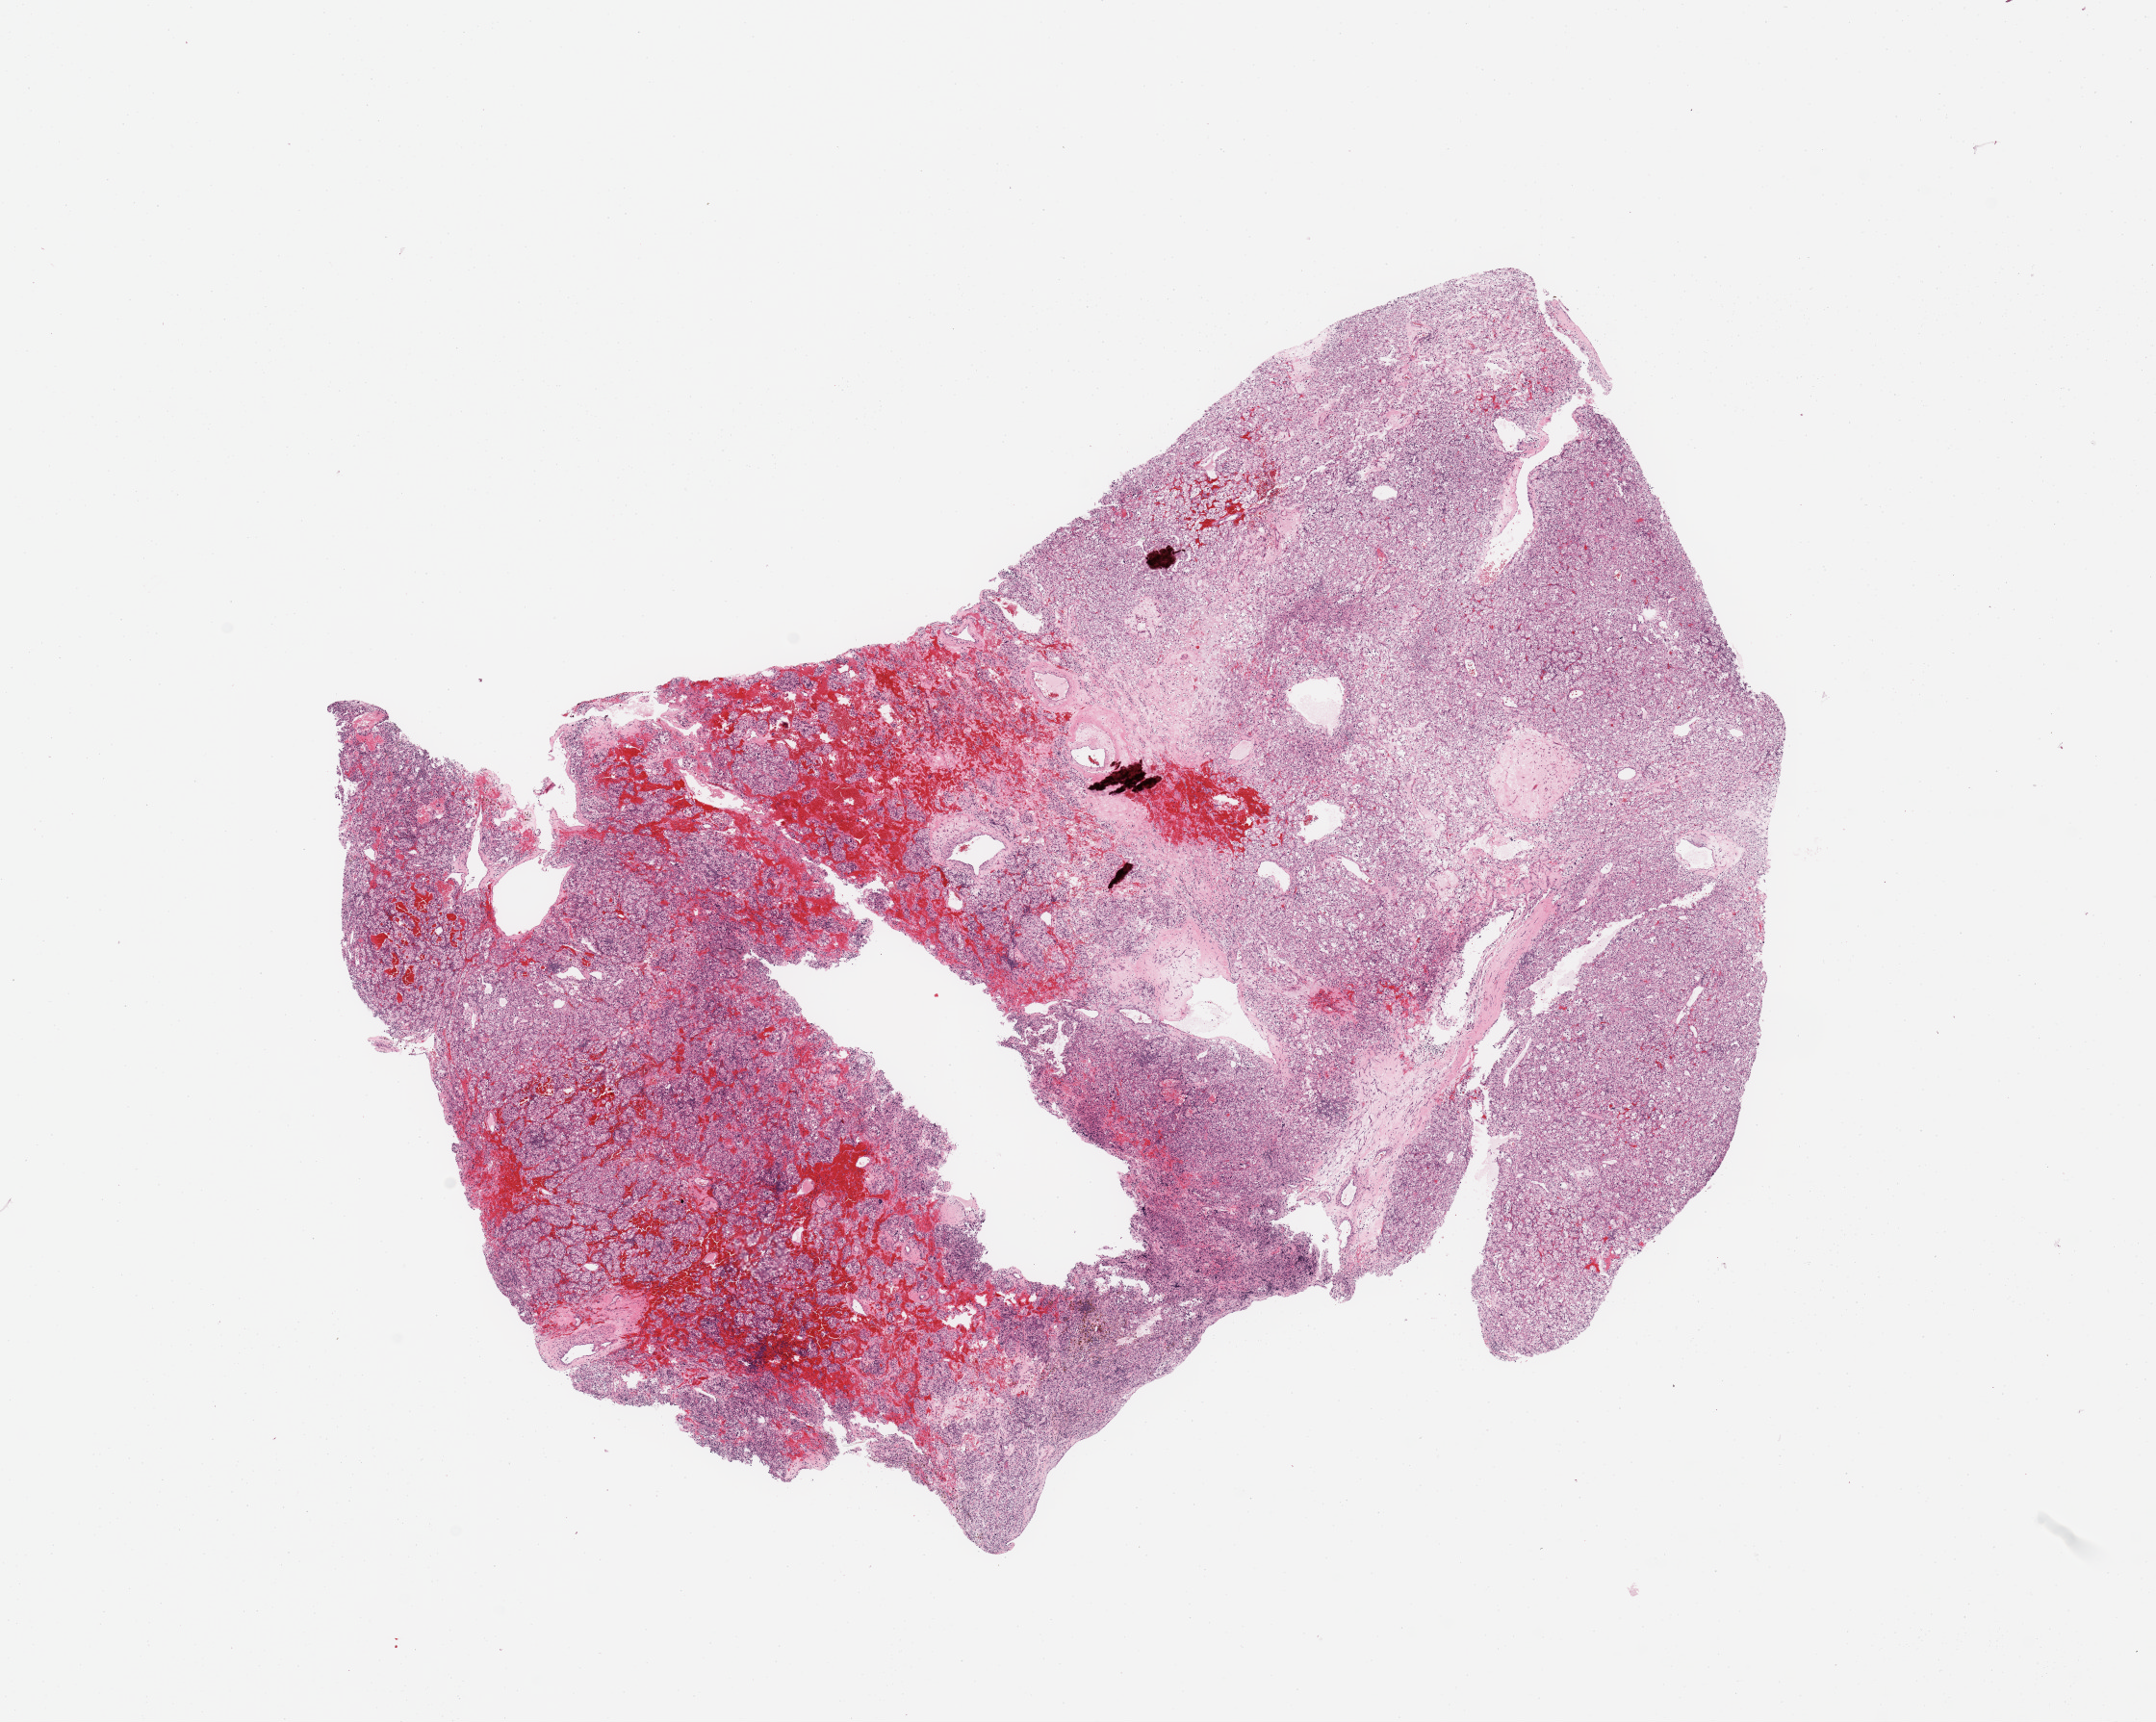
H&E whole-slide image — a low-resolution overview of the entire scanned area, about 17.7 x 14.2 mm (from a 20x scan); tumour tissue sample, sampled site: kidney. Patient: female, age 67 years. Histologic grade: G3 (poorly differentiated). Slide review estimates, as recorded: tumour nuclei 90%, necrosis 5%.
AJCC pathologic stage: I. Histologic diagnosis: Renal cell carcinoma, NOS. Primary tumour site (as recorded): lower pole.